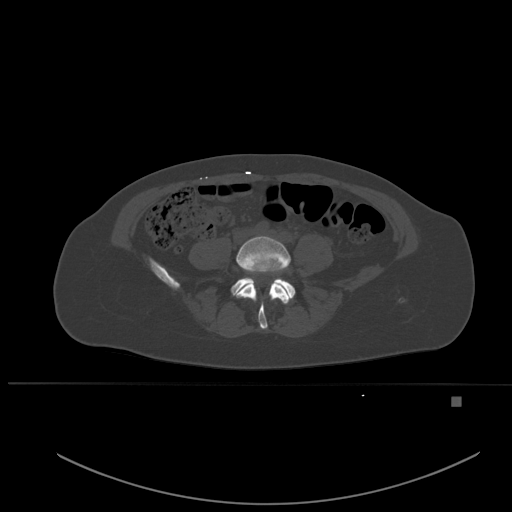
CT including the spine, one axial slice; position 165 of 651 along the scan axis; bone window (W 1800 / L 400 HU); 1.5 mm slice thickness; 512 × 512 image matrix. Patient: female, 49 years. From the clinical record (not read from this slice): primary cancer: breast.
Annotated regions visible in this slice (semi-automatic segmentation, software-assisted and operator-edited):
- L4 vertebra: bounding box [x1, y1, x2, y2] px = [236, 236, 291, 329]
- L5 vertebra: [231, 267, 295, 299]